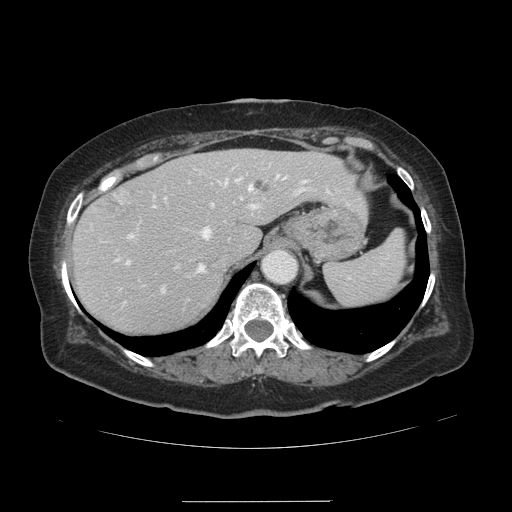
Contrast-enhanced abdominal CT, one axial slice; slice 99 of 141 in the series (ordered by position); 120 kVp; intravenous contrast given; soft-tissue window (W 400 / L 40 HU); 512 × 512 image matrix. Female patient, age 74 years. From the clinical record (not read from this slice): diagnosis: colorectal cancer liver metastases, imaged before liver resection; multiple liver metastases: yes; largest metastasis: 7 cm; disease in both lobes: yes.
Structures marked on this image (outlined manually by an expert reader):
- hepatic veins: box from (x=152, y=175) to (x=304, y=274) px
- liver: (x=75, y=149)–(x=365, y=336)
- planned liver remnant (the part of the liver to remain after resection): (x=75, y=149)–(x=365, y=336)
- portal vein (with intrahepatic branches): (x=127, y=176)–(x=307, y=293)
- liver metastasis: (x=253, y=179)–(x=266, y=192)
- liver metastasis: (x=102, y=186)–(x=133, y=211)